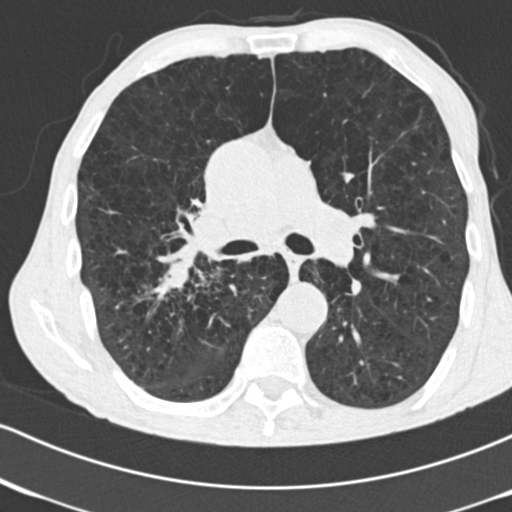
Low-dose screening chest CT, one axial slice; reconstruction kernel B30f; 120 kVp; lung window (W 1500 / L -600 HU); 512 × 512 image matrix.
Annotated regions visible in this slice (outlined manually by an expert reader):
- lesion 1 (tumor, lower lobe of right lung): bounding box <162,255,194,290> (left, top, right, bottom; pixels)